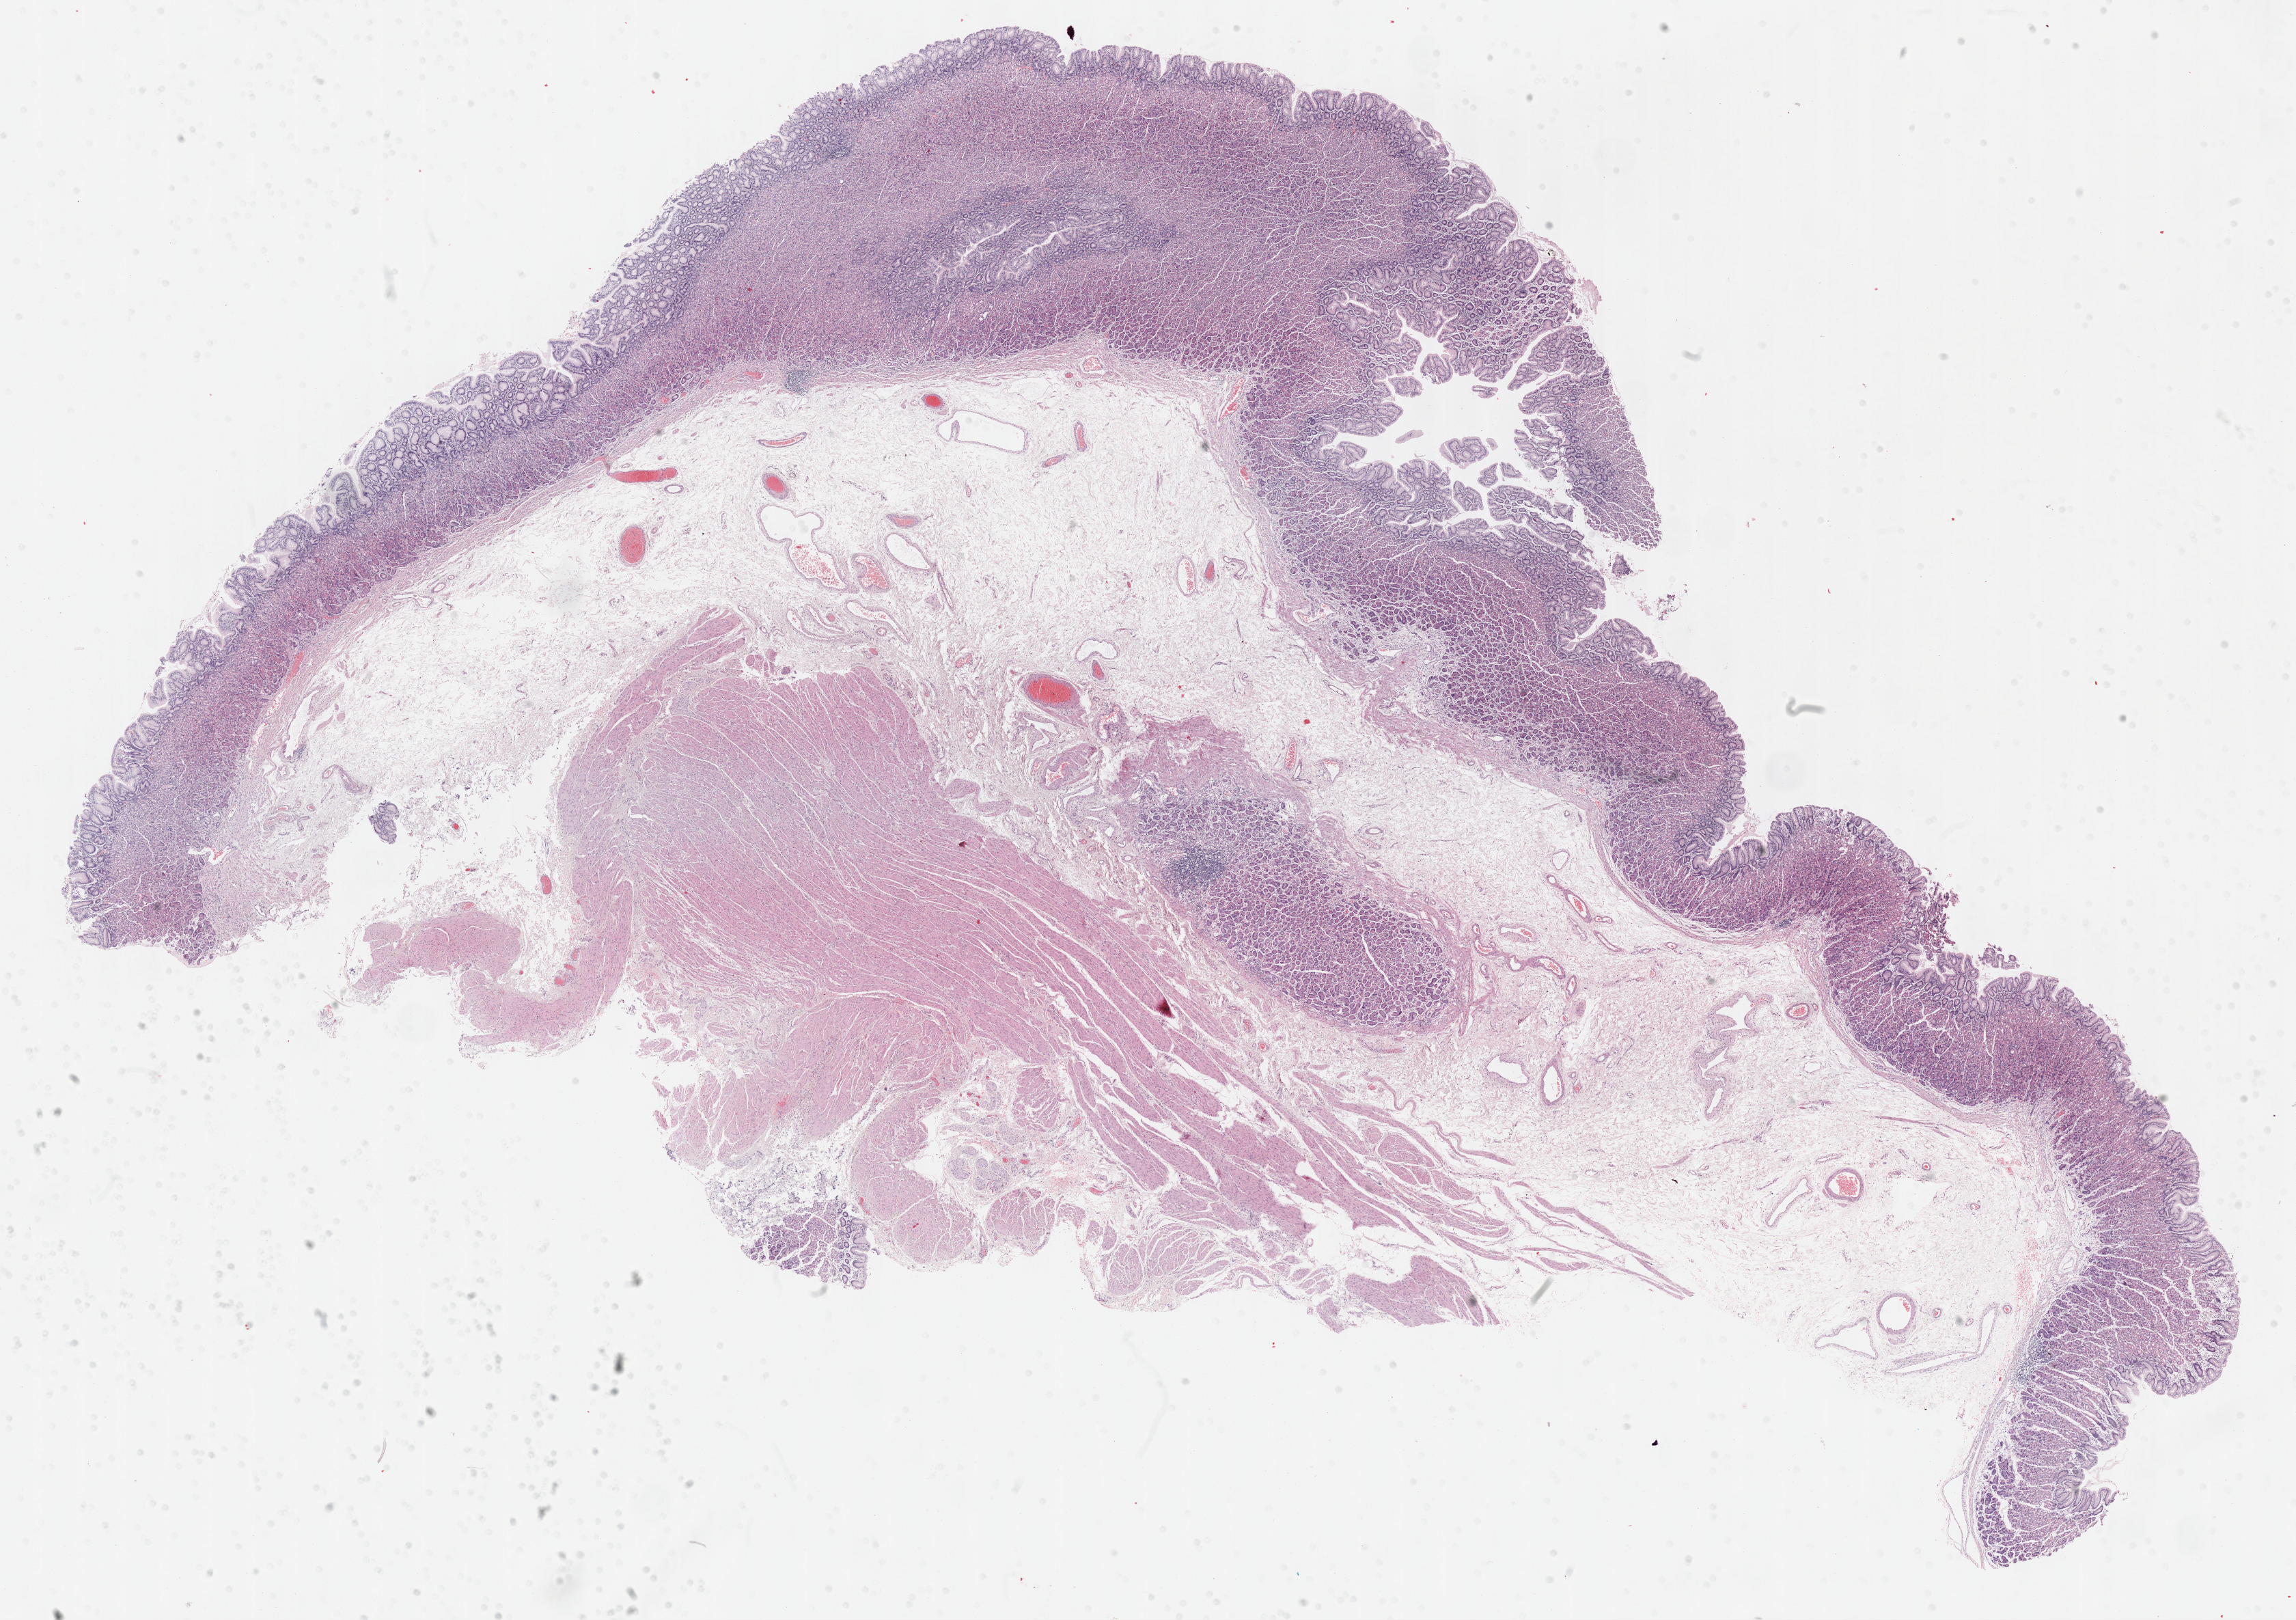
Digitized H&E-stained tissue section (whole slide), low-resolution overview of the scanned area, about 27.2 x 19.2 mm (slide scanned at 40x); formalin-fixed paraffin-embedded (FFPE) diagnostic section; primary tumour sample from the stomach. Female, age 41 years at initial diagnosis. Histologic grade: G3 (poorly differentiated).
AJCC pathologic stage: IV (7th edition). Lymph nodes positive (case pathology): 12 of 16 examined. Diagnosis: Carcinoma, diffuse type (fundus of stomach).